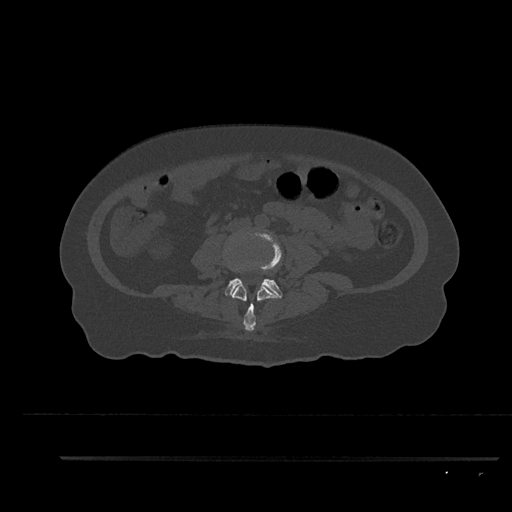
CT including the spine, one axial slice; slice 51 of 797 in the series (ordered by position); reconstruction kernel Br40s/3; bone window (W 1800 / L 400 HU); 0.5 mm slice thickness; 512 × 512 image matrix, field of view 408 × 408 mm. Patient: female, 44 years. Case-level facts recorded for this patient, not image findings: primary cancer: renal.
Annotated regions visible in this slice (semi-automatically segmented with operator editing):
- L3 vertebra: bounding box [x1, y1, x2, y2] px = [232, 285, 282, 331]
- L4 vertebra: [224, 230, 282, 298]